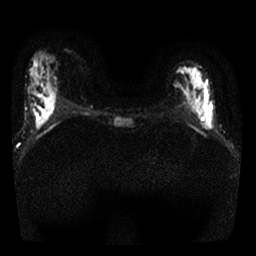
Breast MRI, one axial slice. Position 8 of 25 along the scan axis. Diffusion-weighted series; image 2 of 4 stored at this slice position (different b-values; order by instance number). 1.5 T. 4 mm slice thickness. 256 × 256 image matrix, field of view 300 × 300 mm. Female patient.
Outlined on this slice (manually delineated by an expert):
- tumour on diffusion-weighted imaging: bounding box (x1, y1, x2, y2) in pixels: (175, 65, 214, 130)